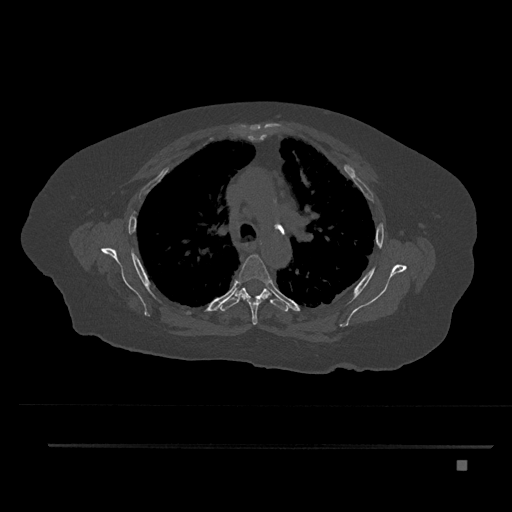
CT including the spine, one axial slice; position 587 of 797 along the scan axis; 120 kVp; bone window (W 1800 / L 400 HU); 0.5 mm slice thickness; 512 × 512 image matrix, field of view 437 × 437 mm. Female patient, age 76 years. Case-level facts recorded for this patient, not image findings: primary cancer: lung.
Annotated regions visible in this slice (semi-automatic segmentation, software-assisted and operator-edited):
- T4 vertebra: bounding box [x1, y1, x2, y2] px = [238, 254, 271, 325]
- T5 vertebra: [219, 282, 289, 312]